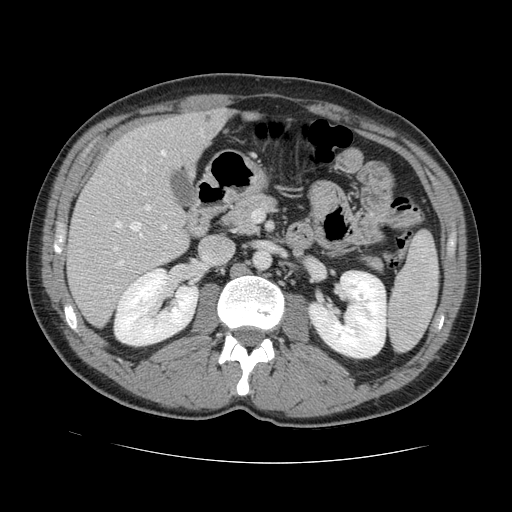
Contrast-enhanced abdominal CT, one axial slice. Slice 65 of 131 in the series (ordered by position). 120 kVp. Soft-tissue window (W 400 / L 40 HU). 512 × 512 image matrix, field of view 380 × 380 mm. Male patient, age 40 years. Case-level facts recorded for this patient, not image findings: diagnosis: colorectal cancer liver metastases, imaged before liver resection; multiple liver metastases: yes; largest metastasis: 2.9 cm; disease in both lobes: yes.
Annotated regions visible in this slice (outlined manually by an expert reader):
- hepatic veins: bounding box [x1, y1, x2, y2] px = [114, 145, 167, 250]
- liver: [68, 111, 226, 326]
- planned liver remnant (the part of the liver to remain after resection): [109, 111, 226, 183]
- portal vein (with intrahepatic branches): [117, 168, 167, 266]
- liver metastasis: [205, 115, 213, 122]